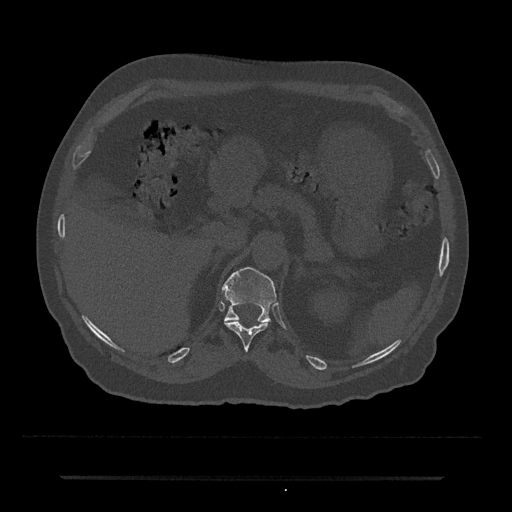
CT including the spine, one axial slice; slice 157 of 797 in the series (ordered by position); reconstruction kernel Br40s/3; bone window (W 1800 / L 400 HU); 512 × 512 image matrix, field of view 437 × 437 mm. Patient: male, 69 years. From the clinical record (not read from this slice): primary cancer: prostate.
Annotated regions visible in this slice (semi-automatic segmentation, software-assisted and operator-edited):
- T11 vertebra: box from (x=225, y=321) to (x=268, y=351) px
- T12 vertebra: (x=222, y=267)–(x=276, y=322)